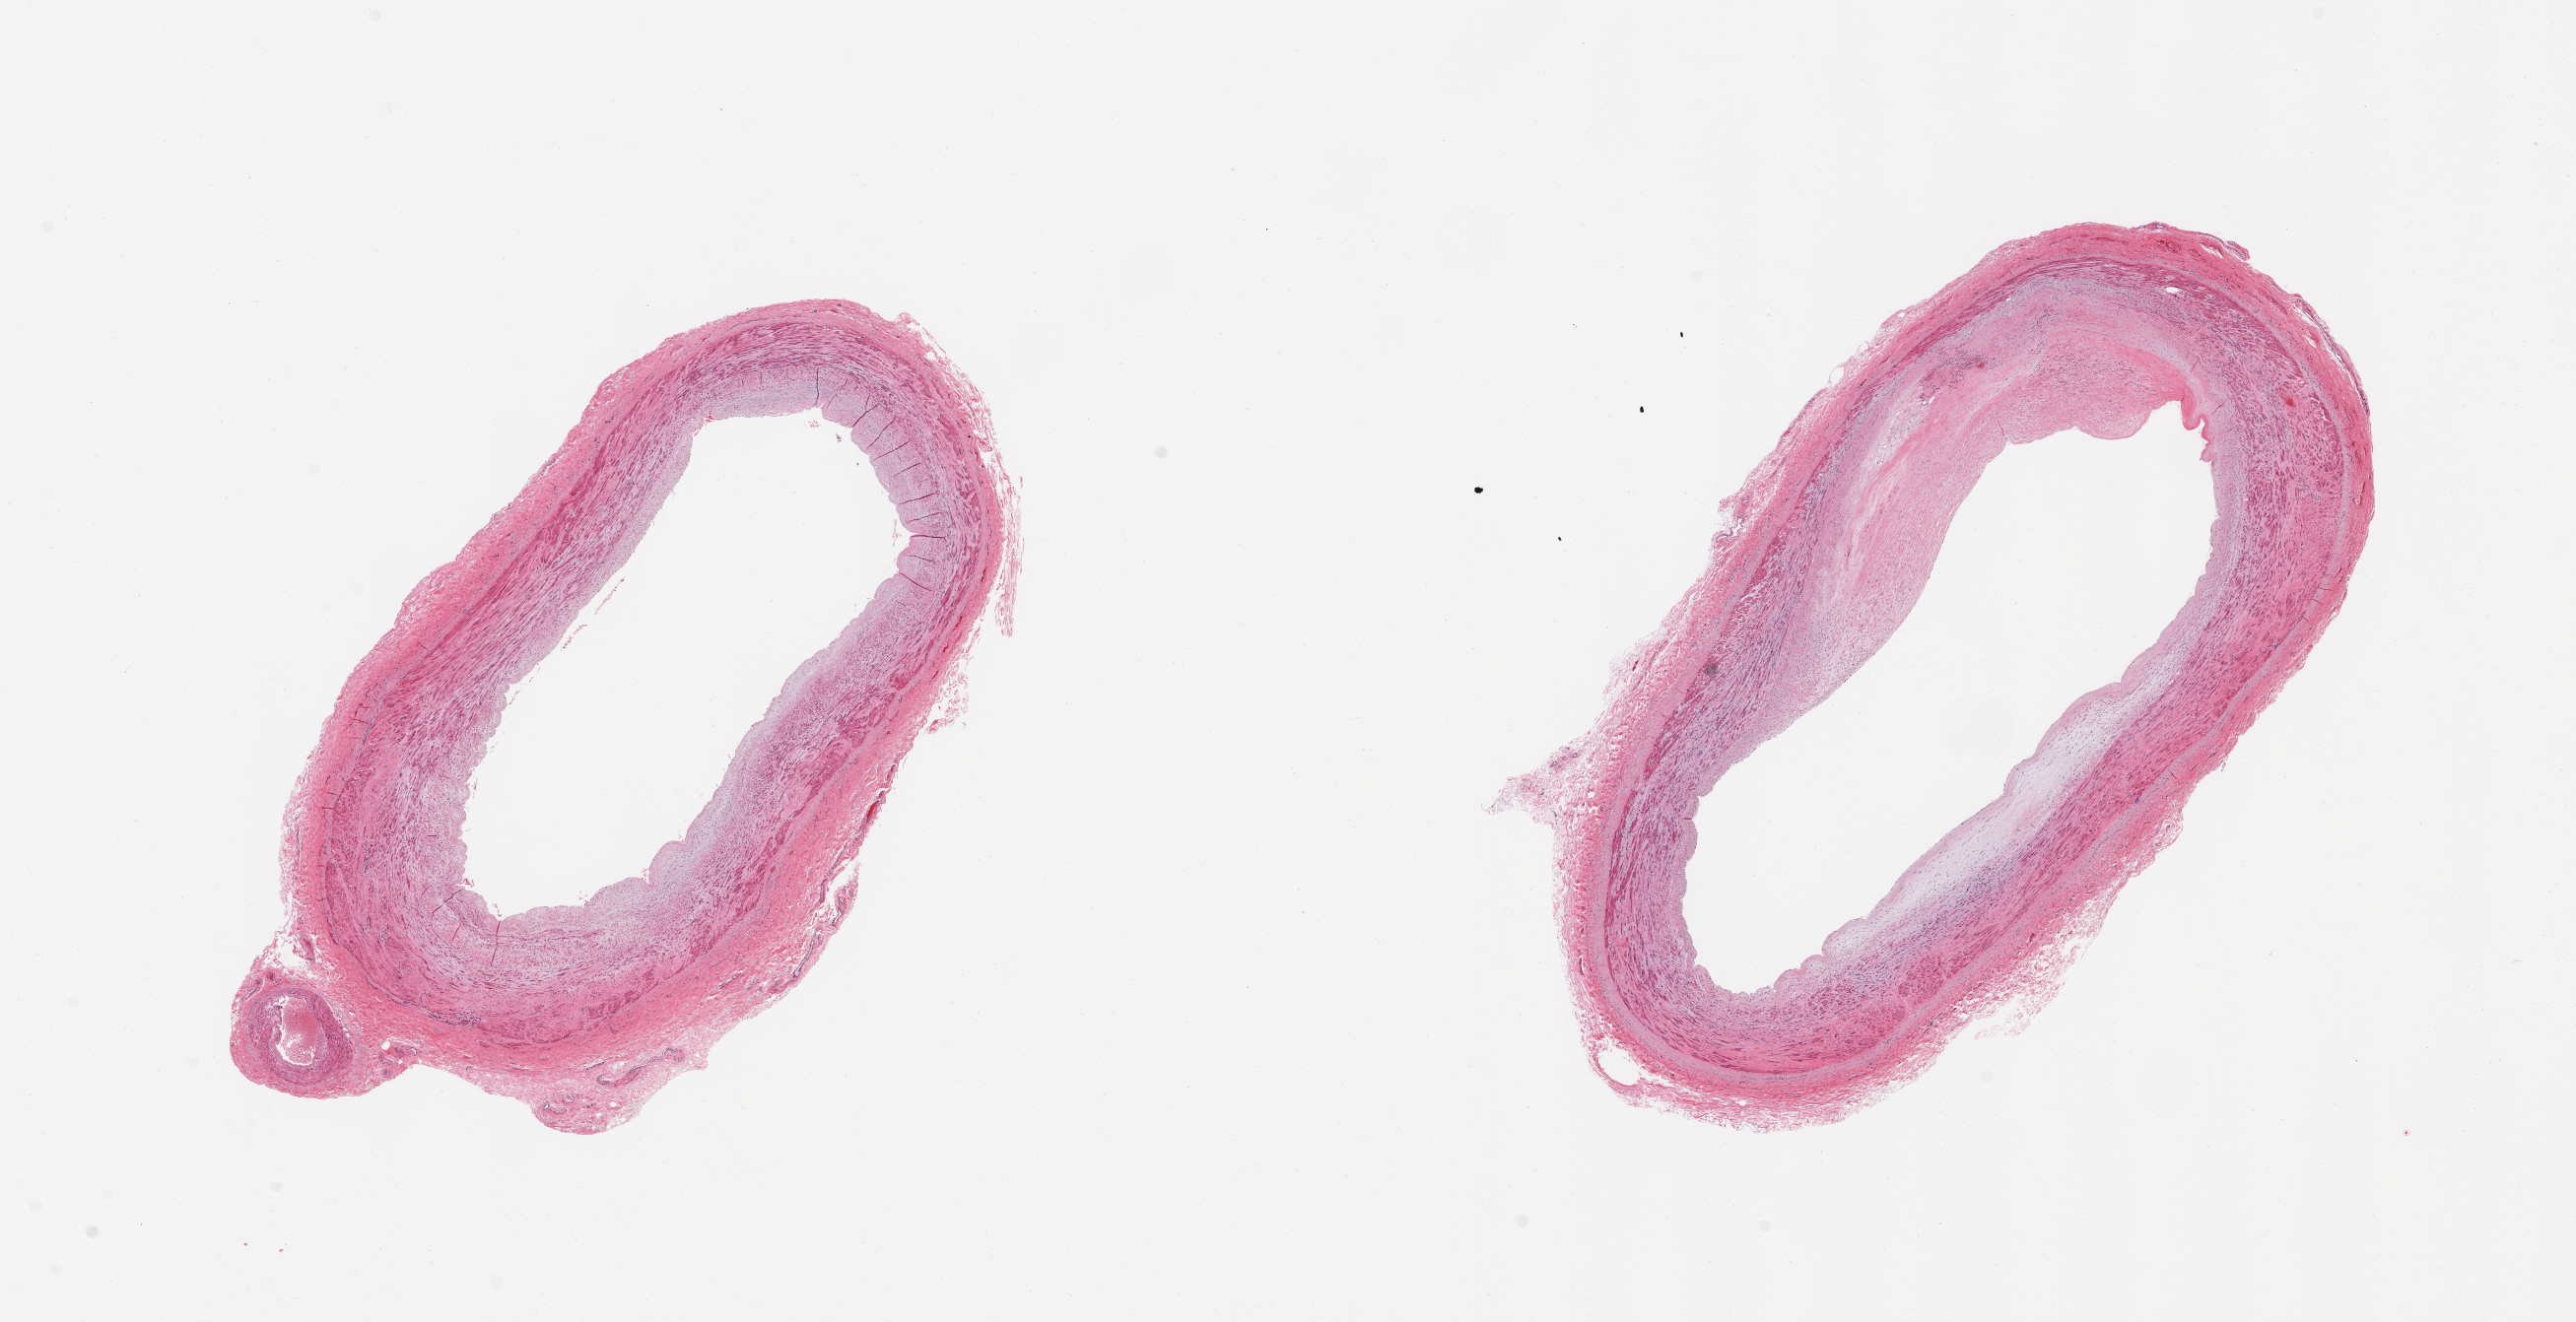
Digitized hematoxylin and eosin (H&E)-stained section, low-resolution overview of the scanned area, about 20.7 x 10.6 mm (slide scanned at 20x); PAXgene-fixed paraffin-embedded (PFPE) section; section of tibial artery (target tissue); donor tissue sample. Donor sex: female.
* review note (as recorded): 2 pieces, no adherent fat; atherosis occludes 30-40% of lumen